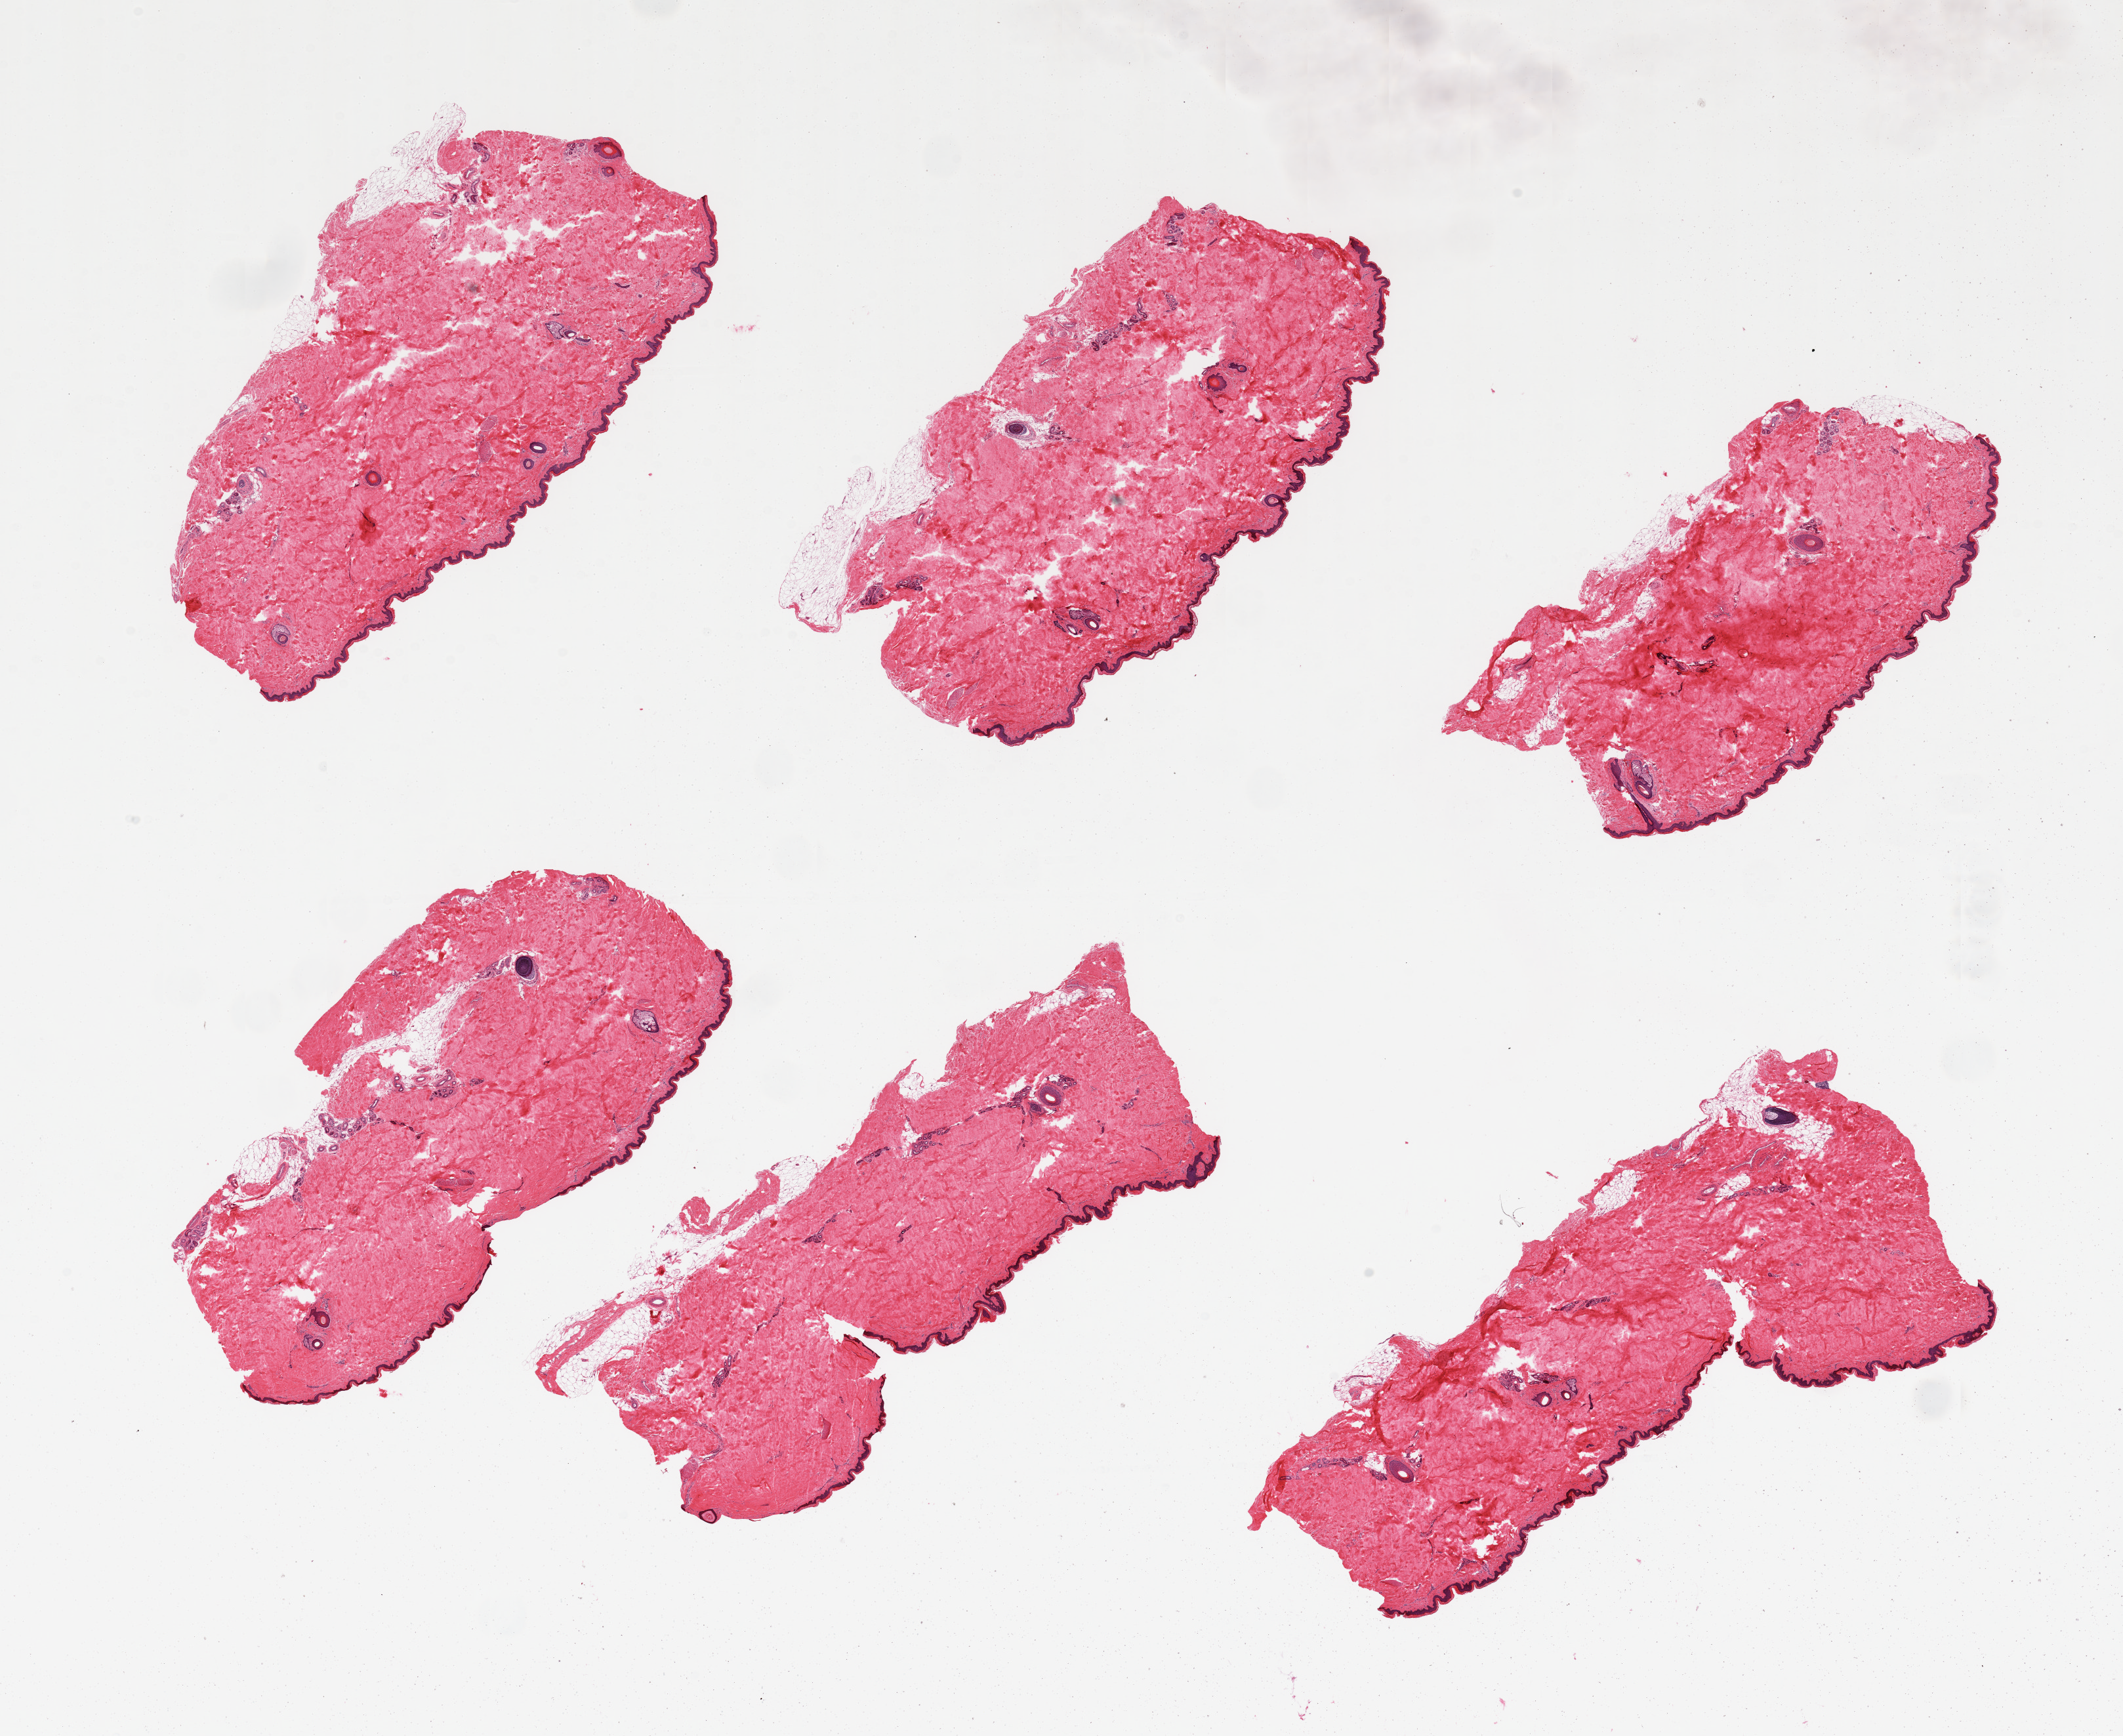
Digitized H&E-stained section — whole scanned area (about 25.6 x 20.9 mm, slide scanned at 20x) shown as a low-resolution overview; PAXgene-fixed paraffin-embedded (PFPE) section; target tissue: skin of lower leg; donor tissue sample. Donor: male.
- pathologist's review note for this sample: 6 pieces; well trimmed